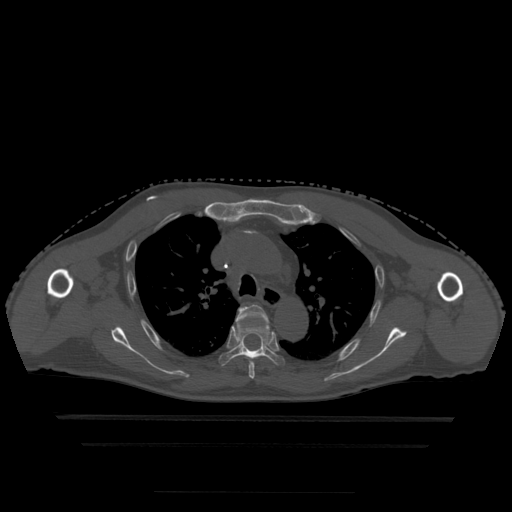
CT including the spine, one axial slice; position 343 of 522 along the scan axis; bone window (W 1800 / L 400 HU); 1.25 mm slice thickness; 512 × 512 image matrix, field of view 436 × 436 mm. Patient age 68 years. From the clinical record (not read from this slice): primary cancer: urothelial.
Annotated regions visible in this slice (semi-automatically segmented with operator editing):
- T4 vertebra: box from (x=236, y=305) to (x=269, y=379) px
- T5 vertebra: (x=219, y=321)–(x=285, y=366)